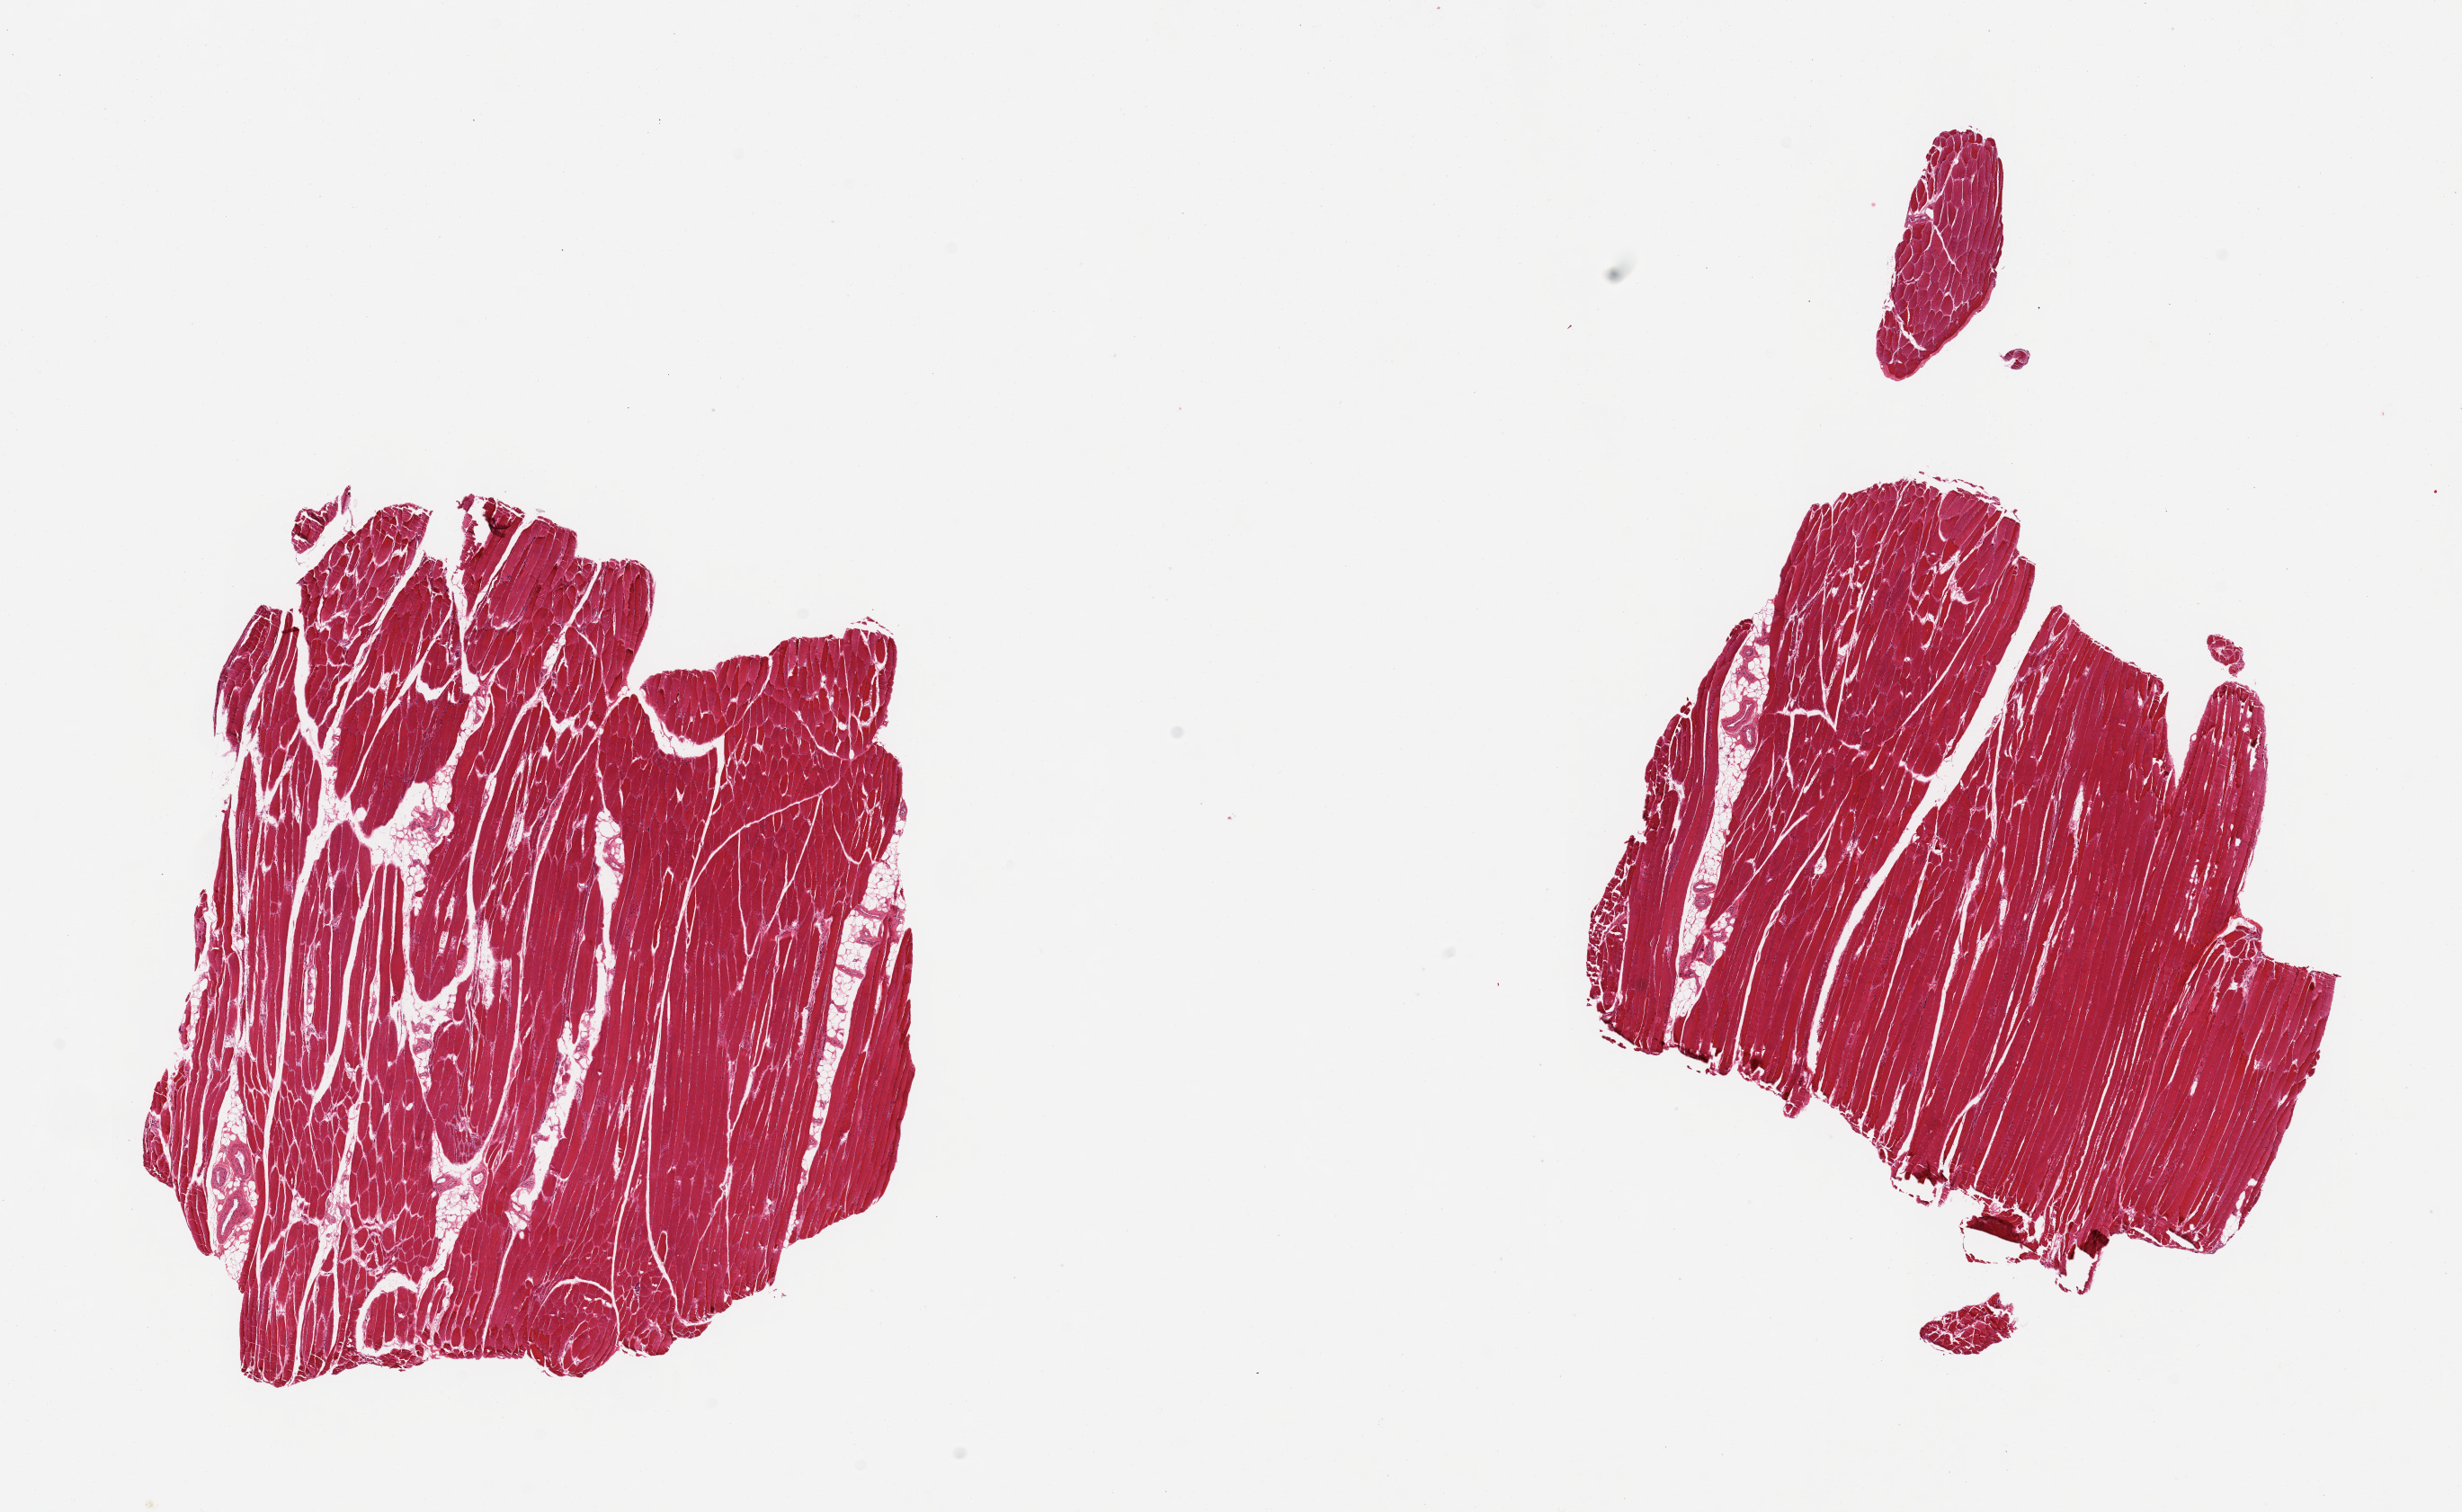
Whole-slide image, H&E stain, shown as a low-resolution overview of the whole scanned area (about 21.7 x 13.3 mm, from a 20x scan), PAXgene-fixed paraffin-embedded (PFPE) section, section of skeletal muscle (target tissue), tissue donor sample.
Pathologist's review note for this sample: 2 pieces; some atrophy, 5-10% internal fat.